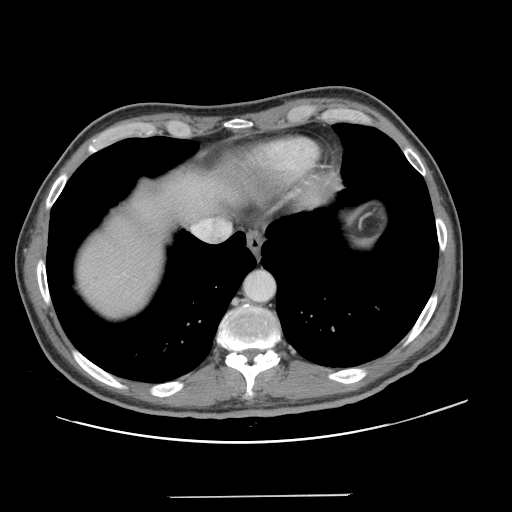
Contrast-enhanced abdominal CT, one axial slice. Position 118 of 131 along the scan axis. 120 kVp. Intravenous contrast given. Soft-tissue window (W 400 / L 40 HU). 512 × 512 image matrix, field of view 403 × 403 mm. Male patient, age 60 years. Case-level facts recorded for this patient, not image findings: diagnosis: colorectal cancer liver metastases, imaged before liver resection; multiple liver metastases: no; largest metastasis: 2.5 cm.
Annotated regions visible in this slice (outlined manually by an expert reader):
- liver: bounding box <75,142,309,318> (left, top, right, bottom; pixels)
- planned liver remnant (the part of the liver to remain after resection): <75,145,308,318>